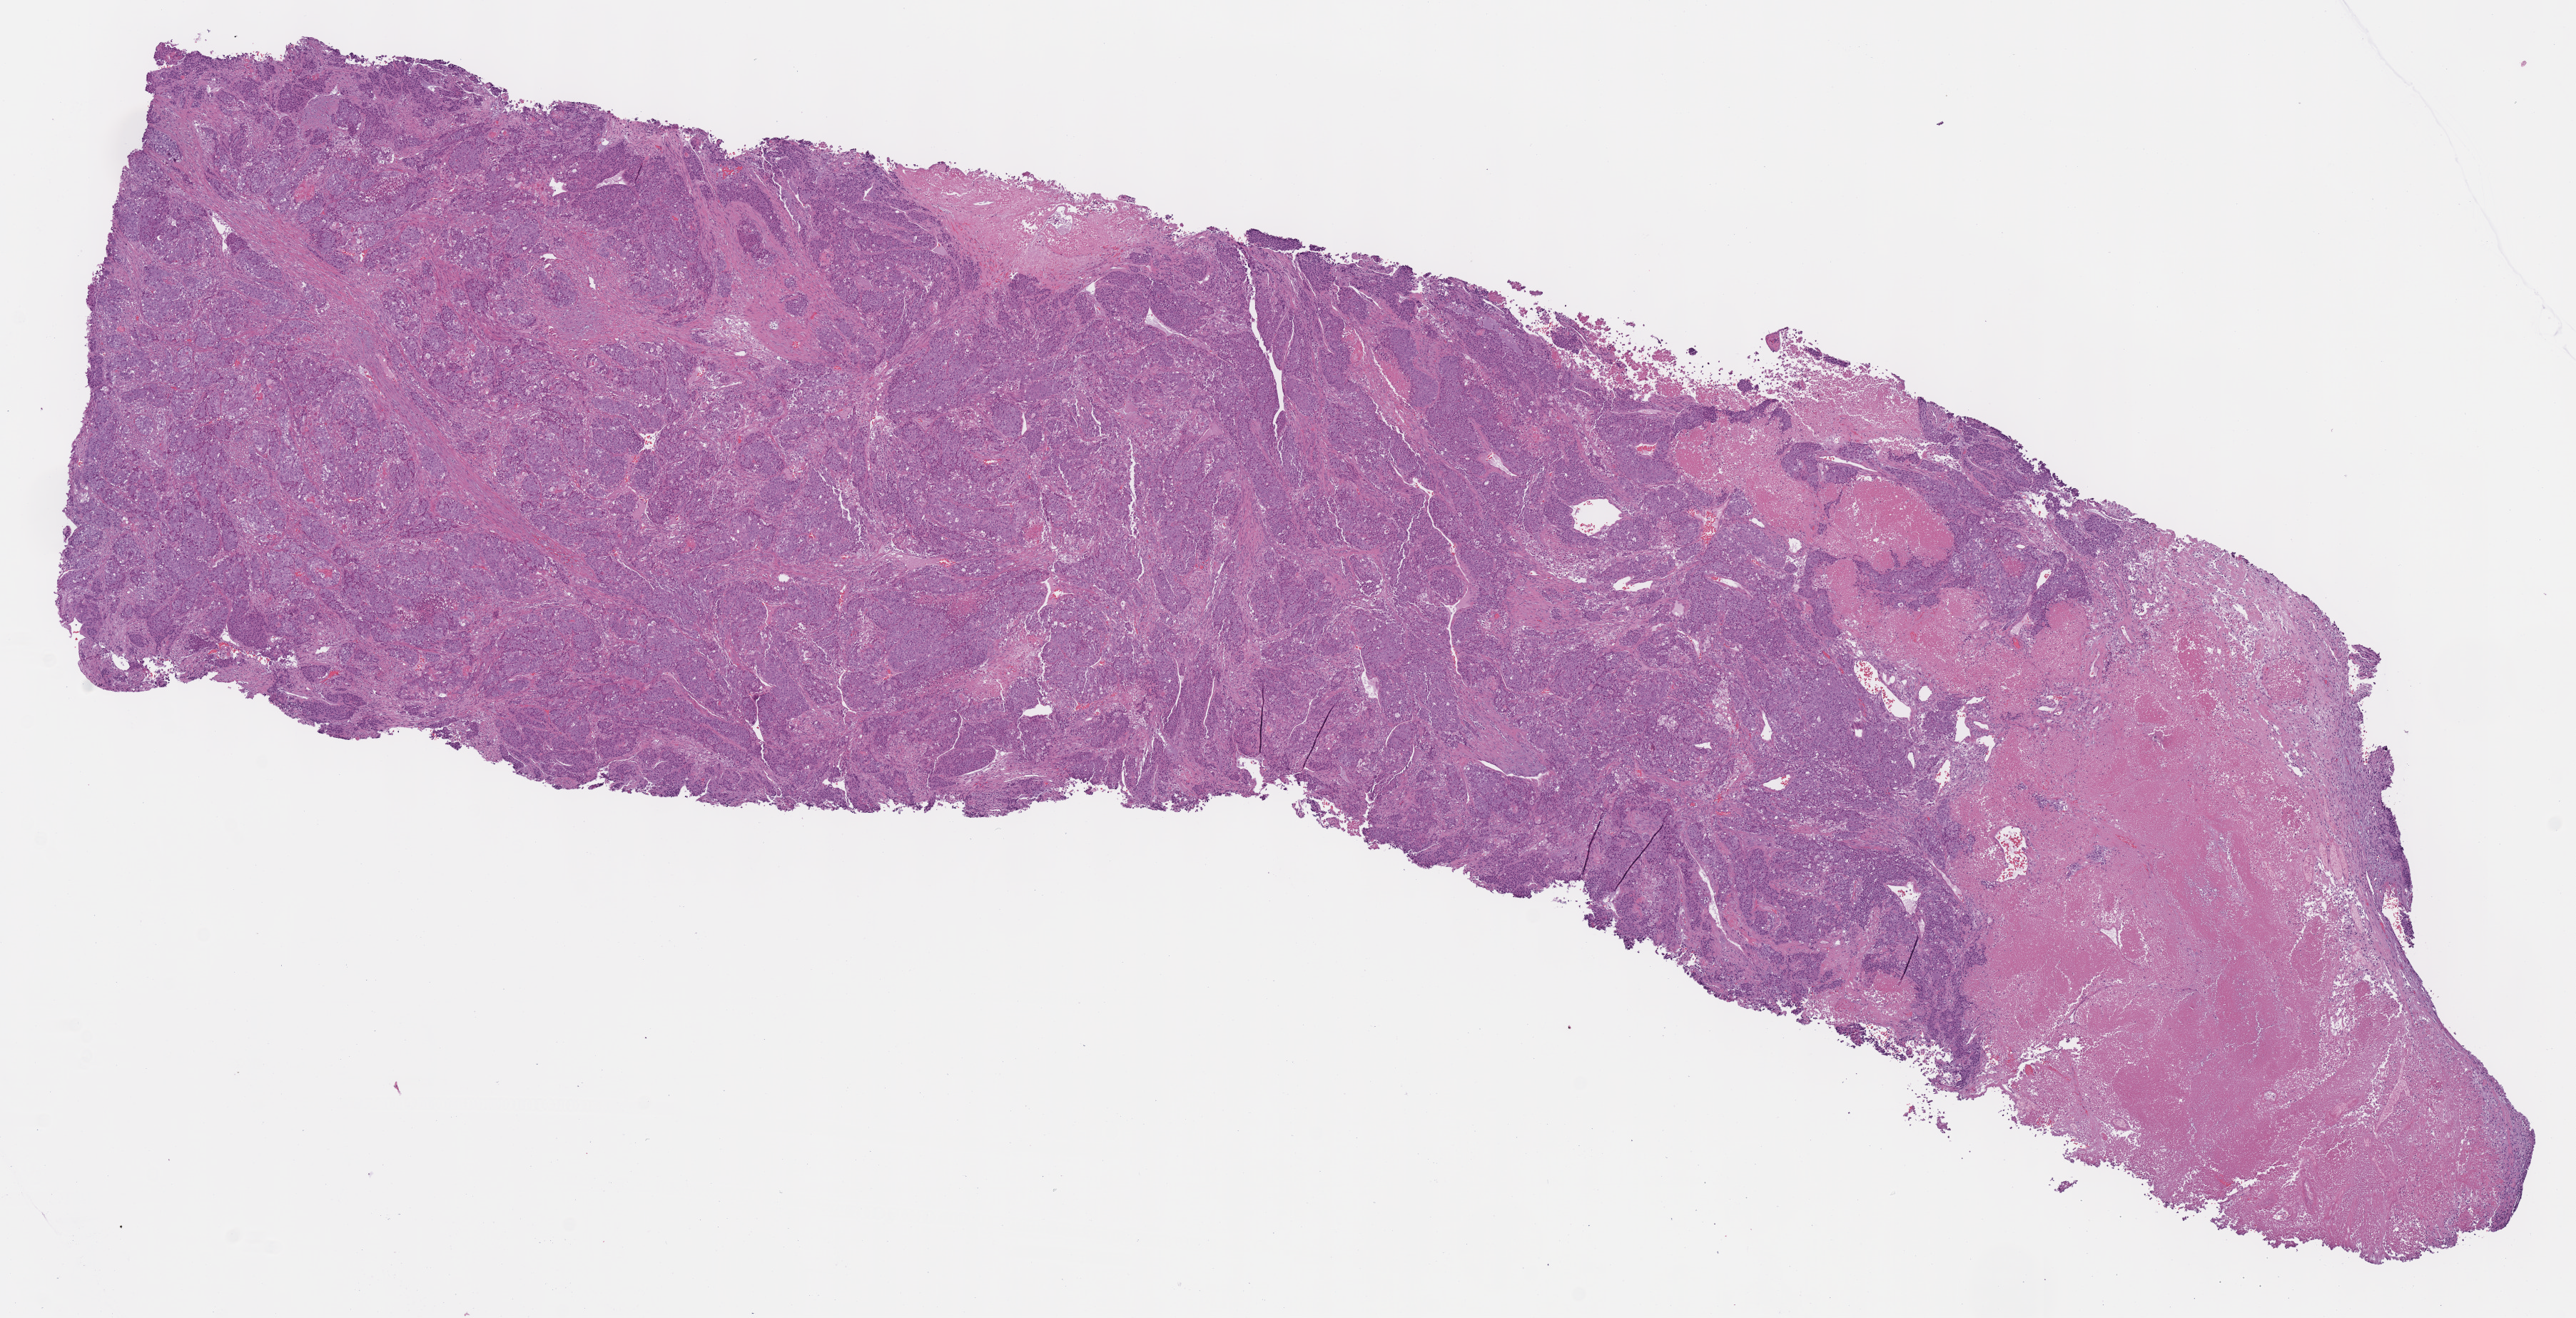
H&E-stained whole-slide image — low-resolution overview of the scanned area, about 14.2 x 7.3 mm (acquisition: 40x scan), formalin-fixed paraffin-embedded (FFPE) diagnostic section, primary tumour sample from the cervix. Female, age 64 years at initial diagnosis. Histologic grade: G3 (poorly differentiated).
- FIGO stage: IIA2
- diagnosis: Squamous cell carcinoma, large cell, nonkeratinizing, NOS
- lymph nodes positive (case pathology): 0 of 9 examined